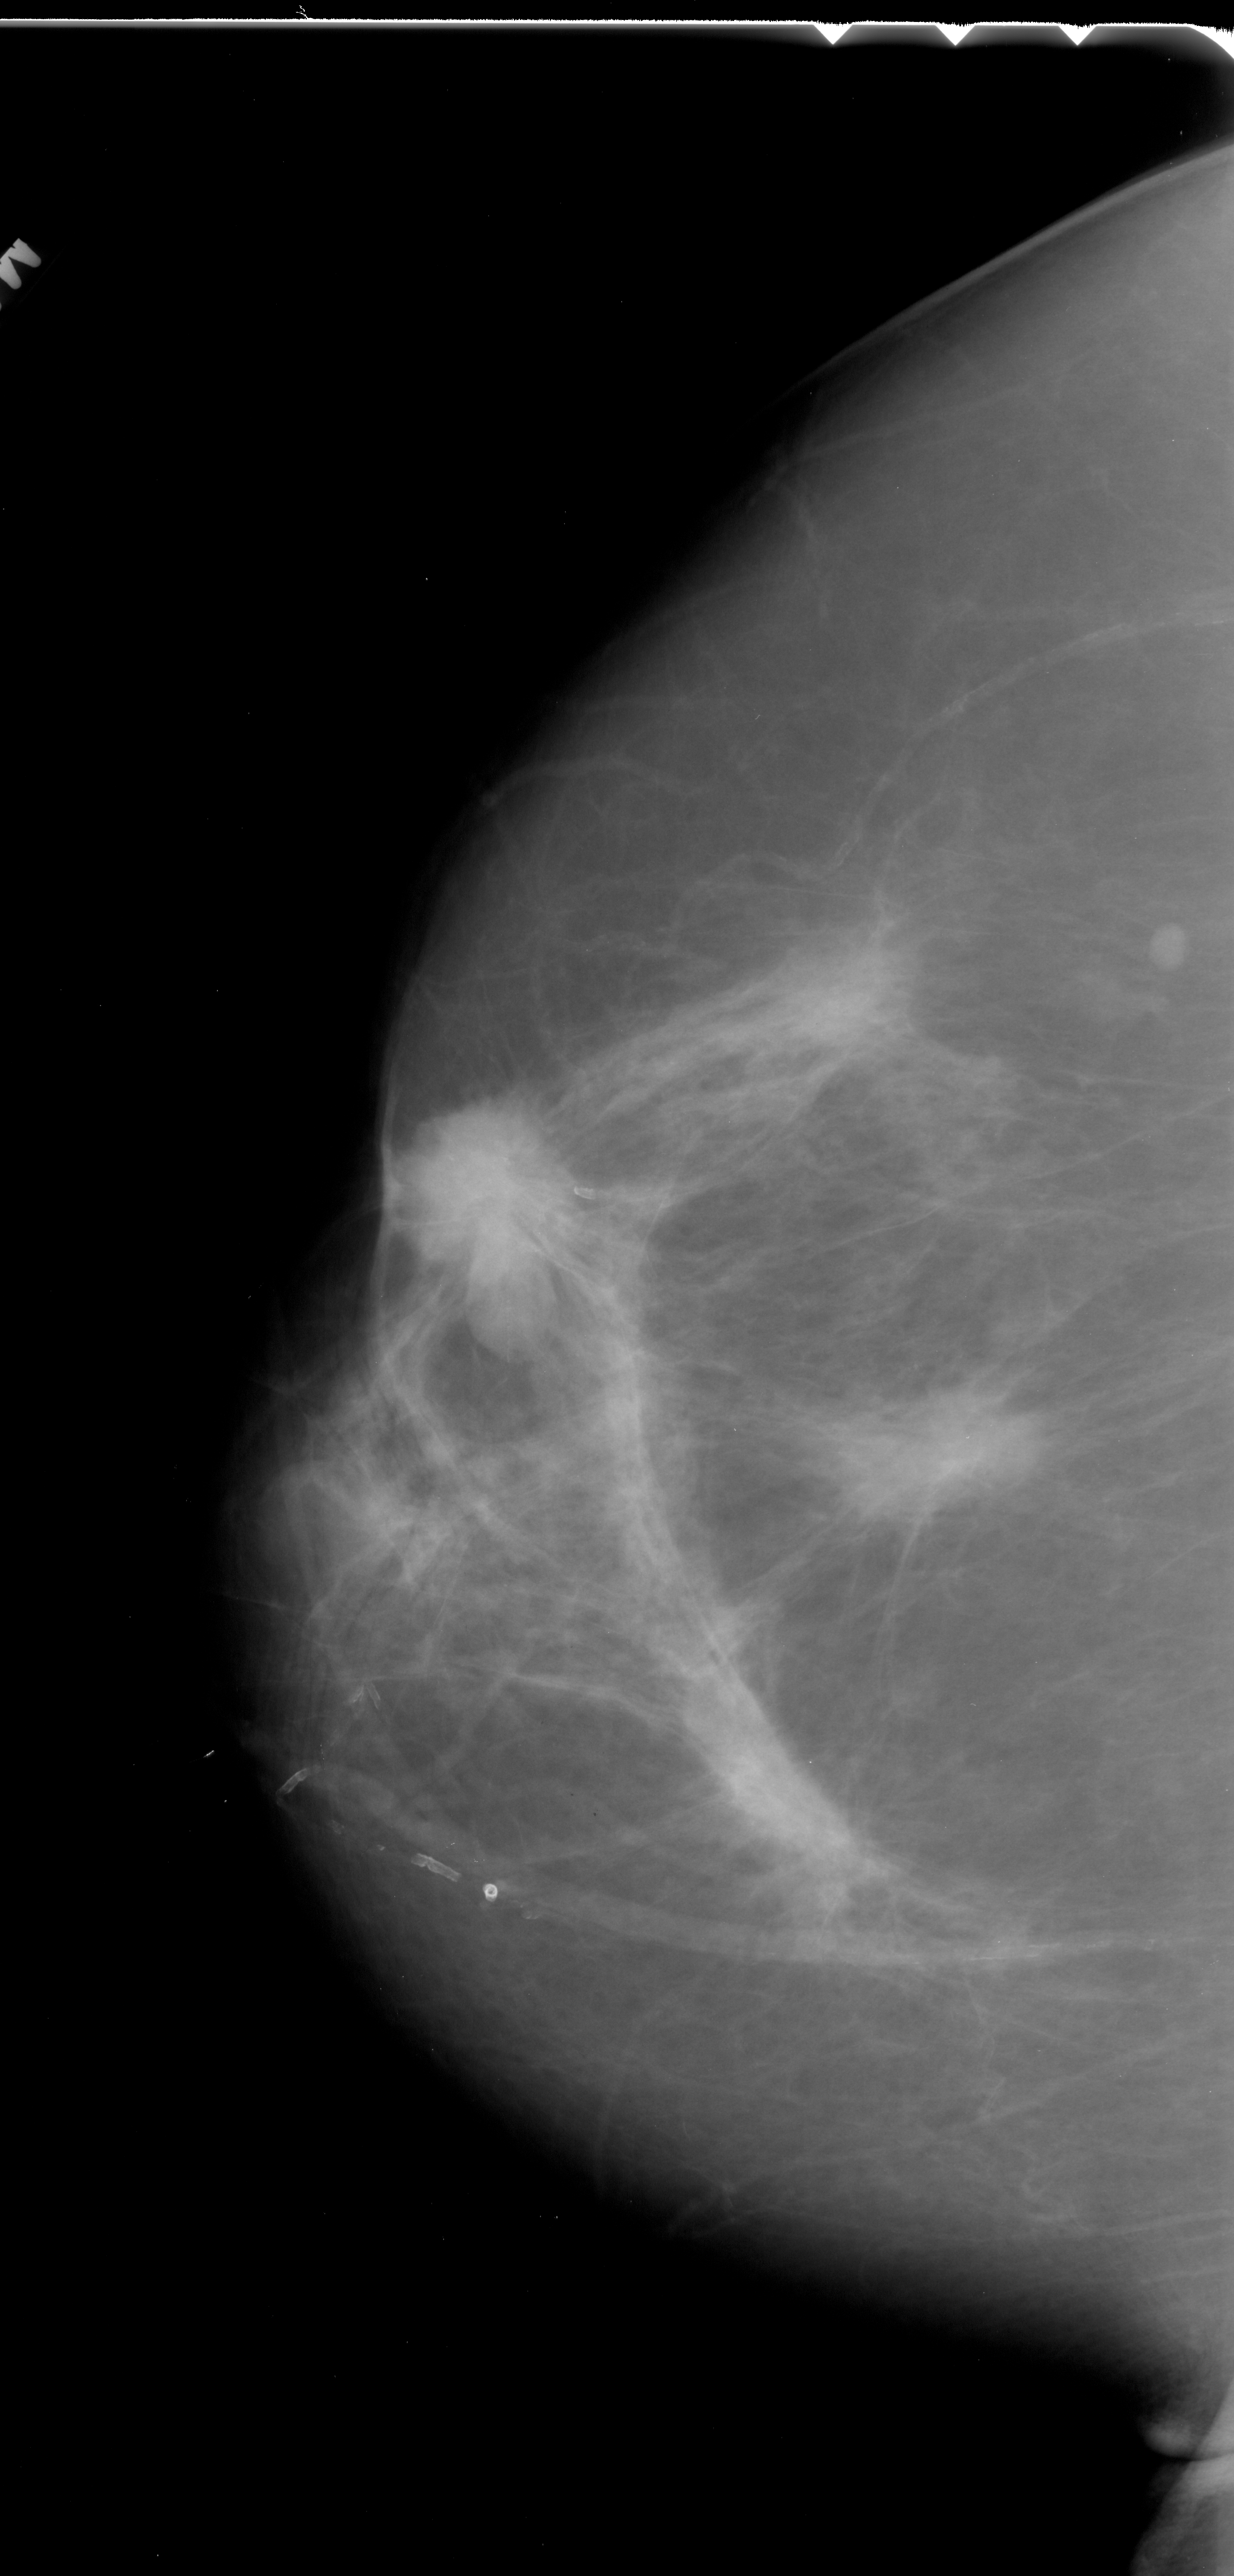
Scanned film-screen mammogram; left breast; CC view.
Radiologist-marked abnormalities on this image: Finding 1 of 2: mass, shape round, margins spiculated; BI-RADS assessment category 5; subtlety rating 5 on a 1 (subtle) to 5 (obvious) scale; pathology result (as recorded, not read from the image): malignant. Finding 2 of 2: mass, shape irregular, margins spiculated; BI-RADS assessment category 5; pathology result (as recorded, not read from the image): malignant.